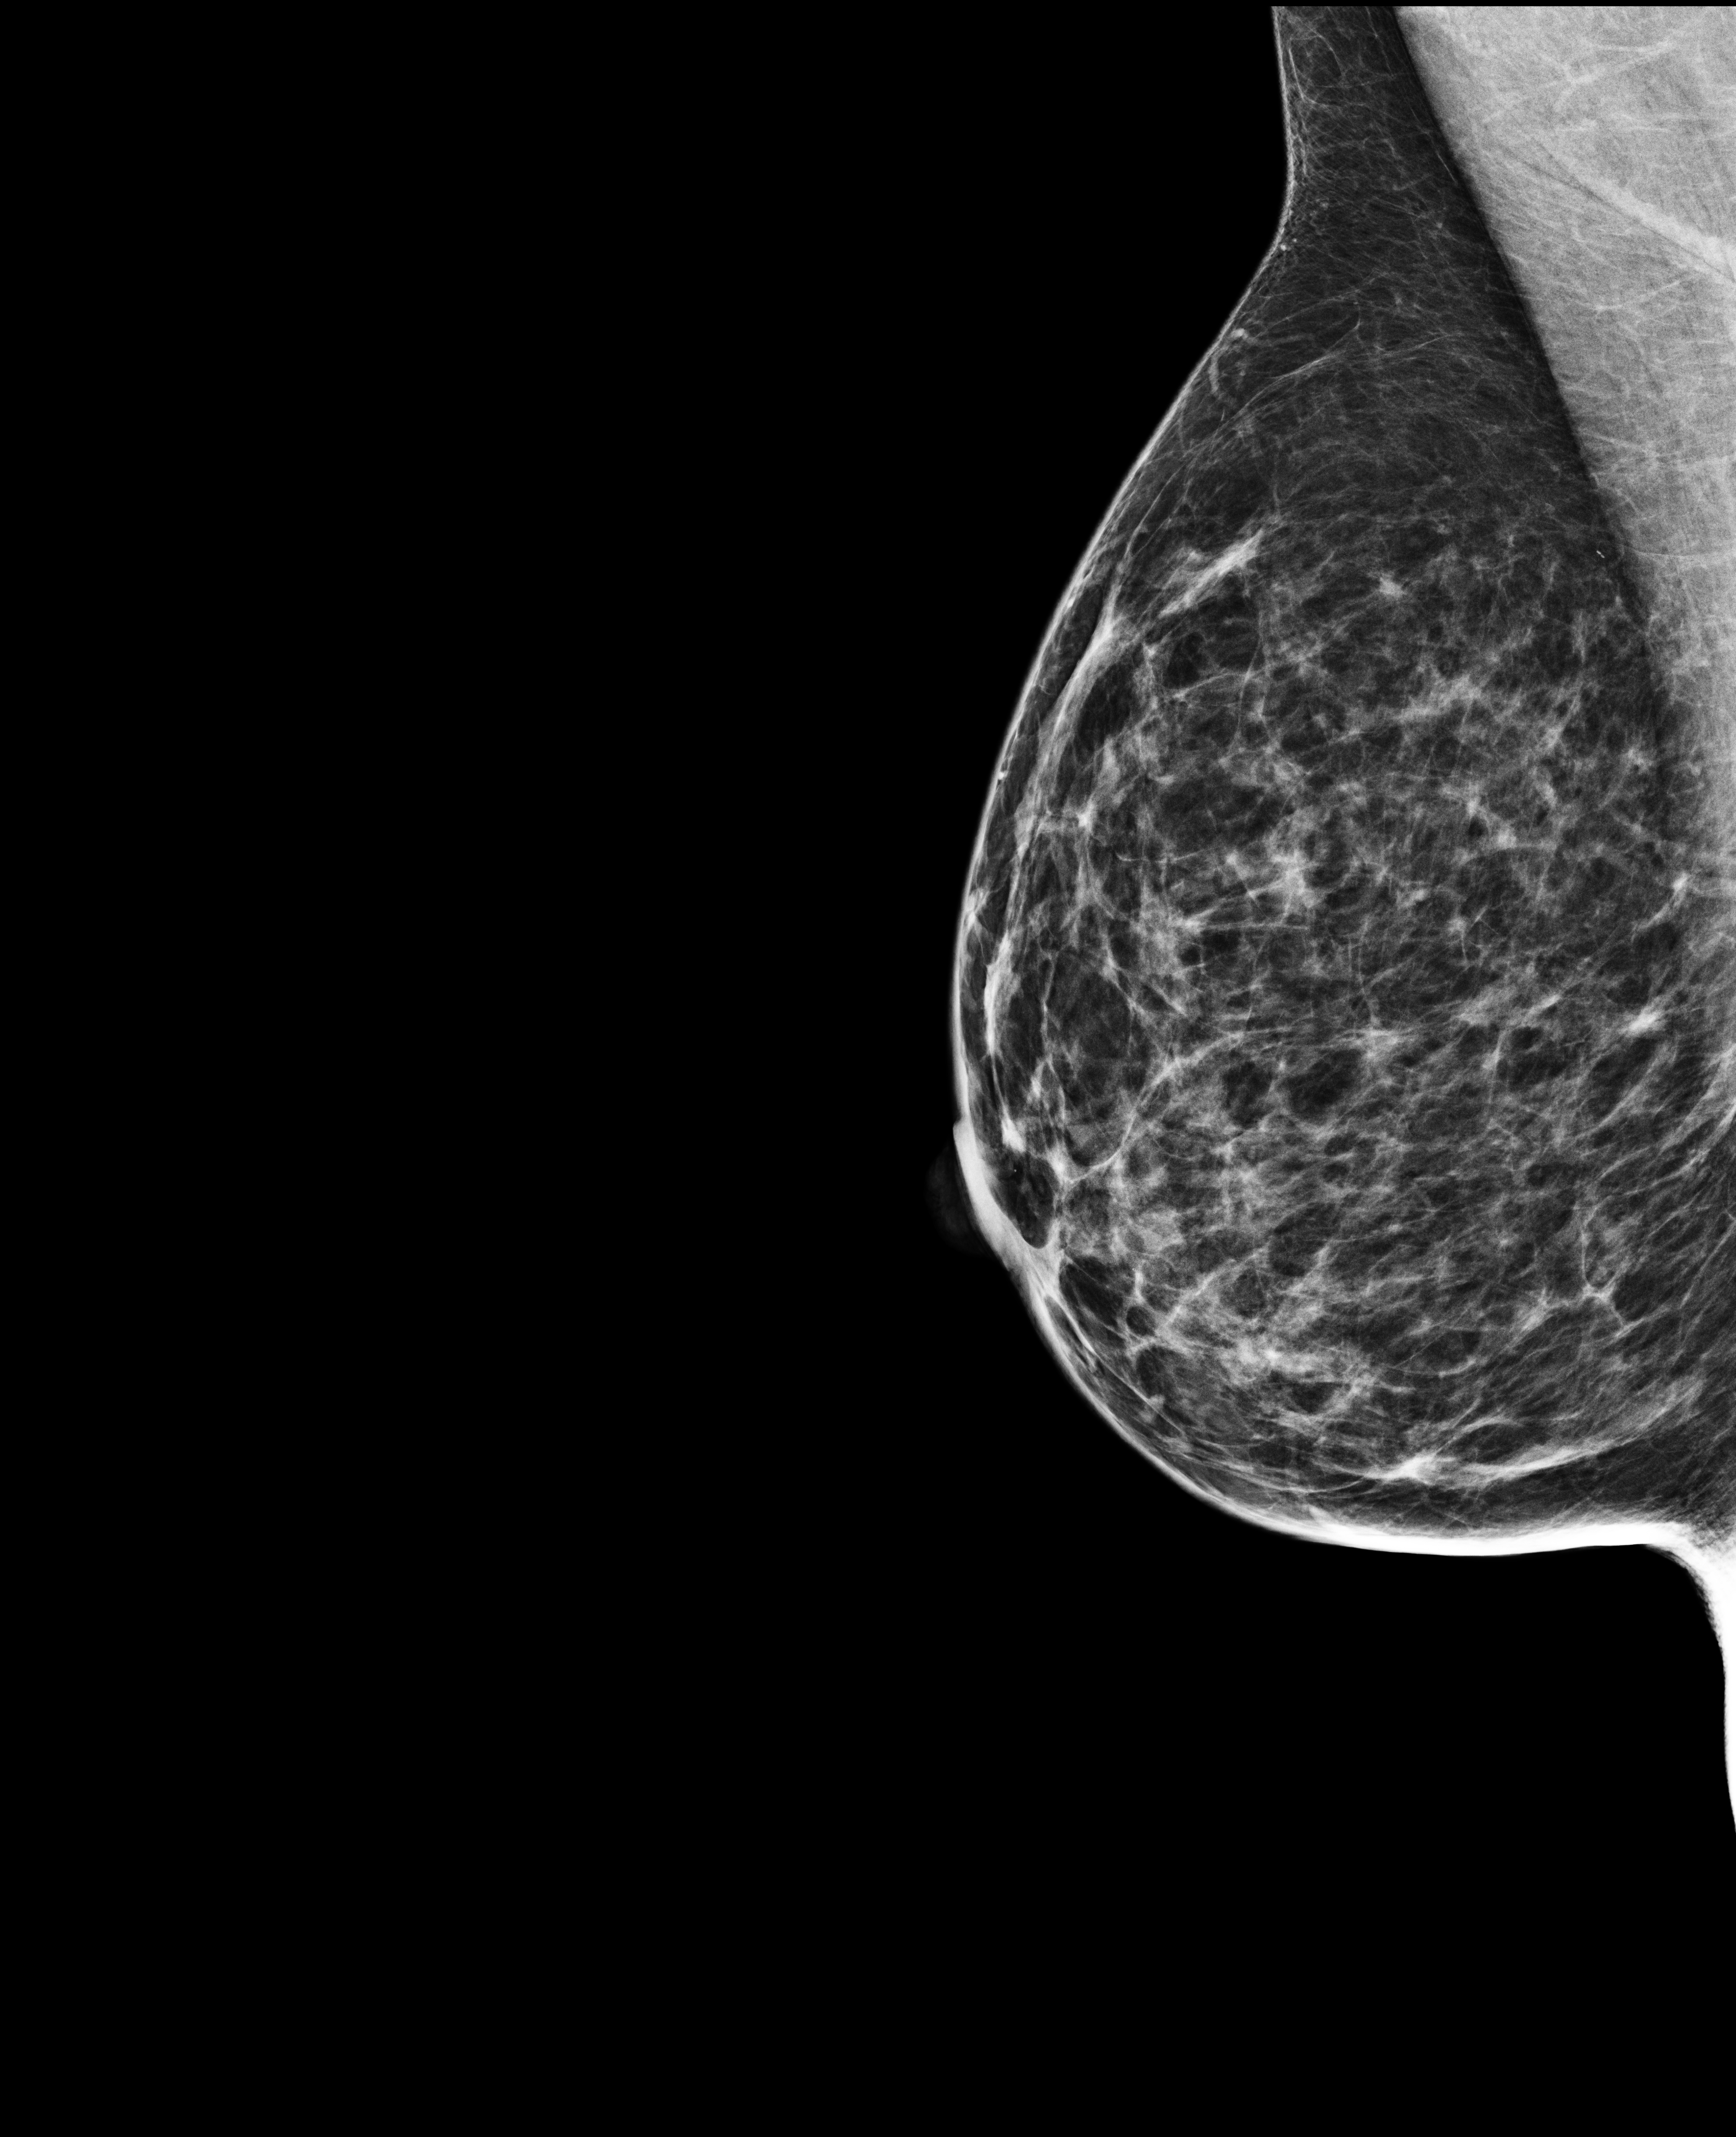
Full-field digital mammogram (FFDM), right breast, mediolateral oblique (MLO) view, annual screening mammography examination, compressed breast thickness 55 mm. Patient: female, 48 years.
Final BI-RADS assessment for this screening round (tomosynthesis exam, both breasts): category 1.